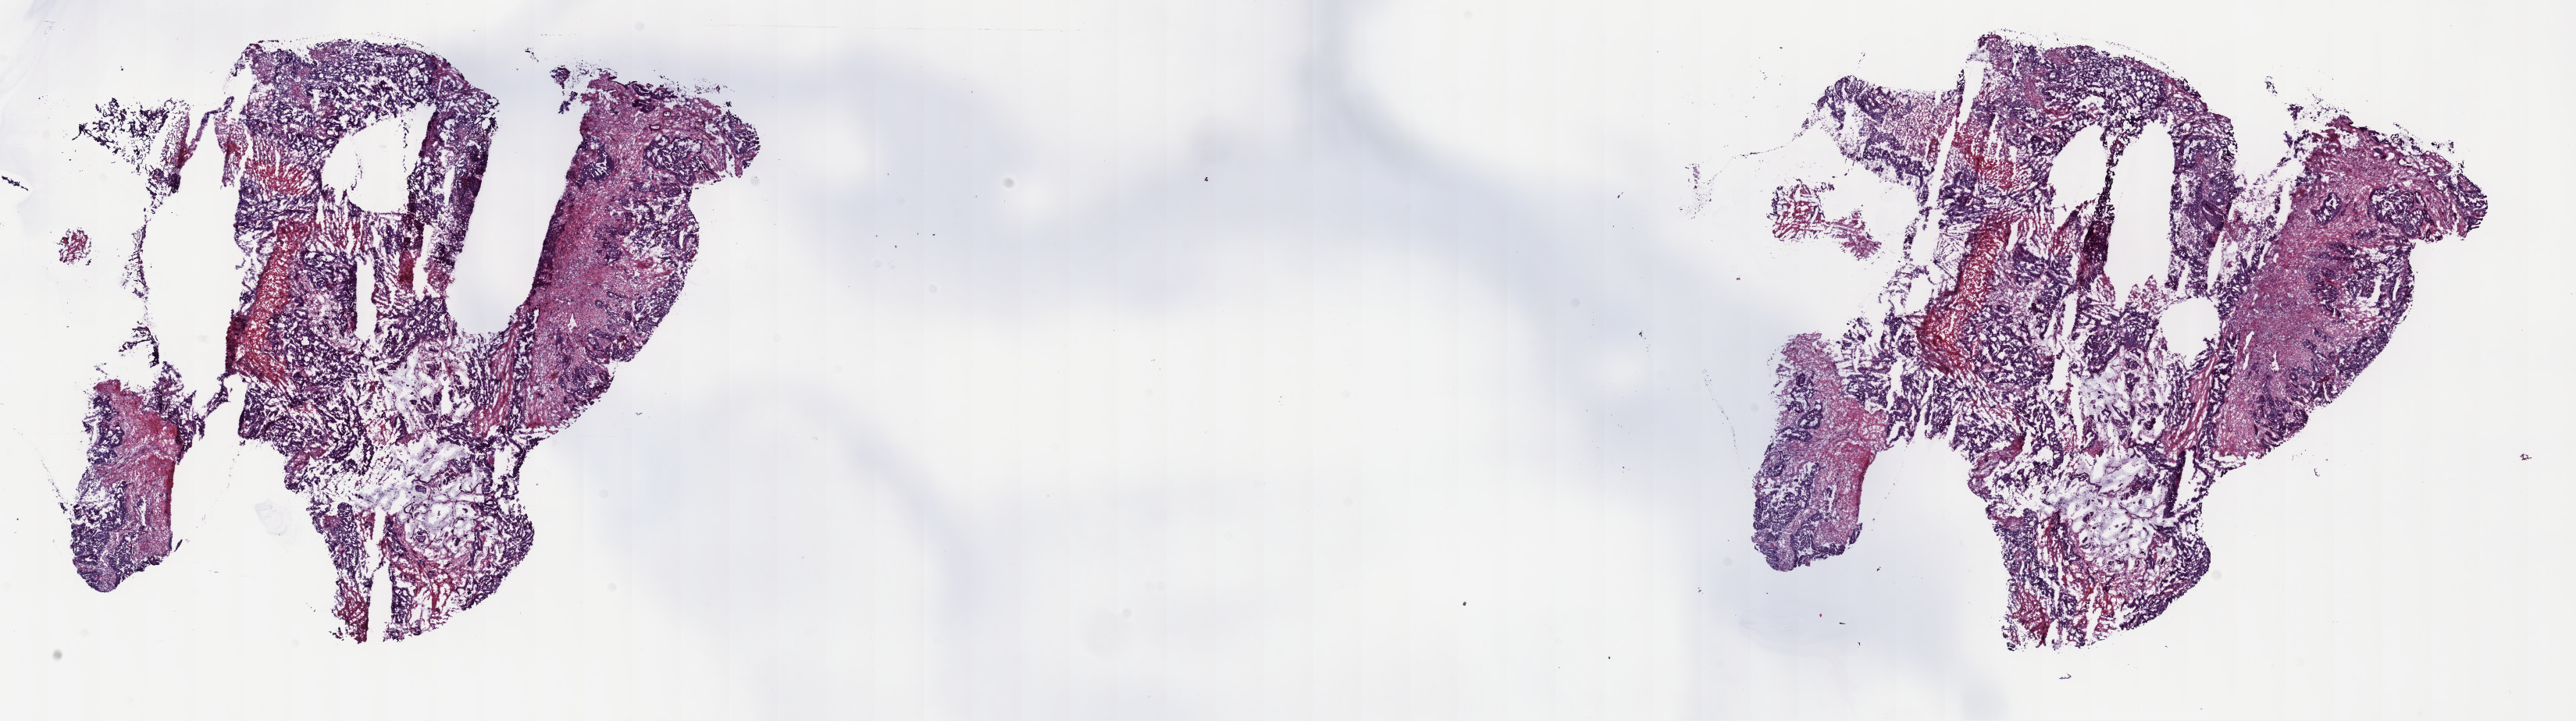
H&E whole-slide image, low-resolution overview of the scanned area, about 26.7 x 7.5 mm (acquisition: 40x scan); frozen section from the top of the tissue portion; colon, primary tumour sample. Male patient; age at initial diagnosis 74 years. Composition of this section per pathologist review: tumour cells 70%, tumour nuclei 70%.
Histologic diagnosis: Adenocarcinoma, NOS (ascending colon).